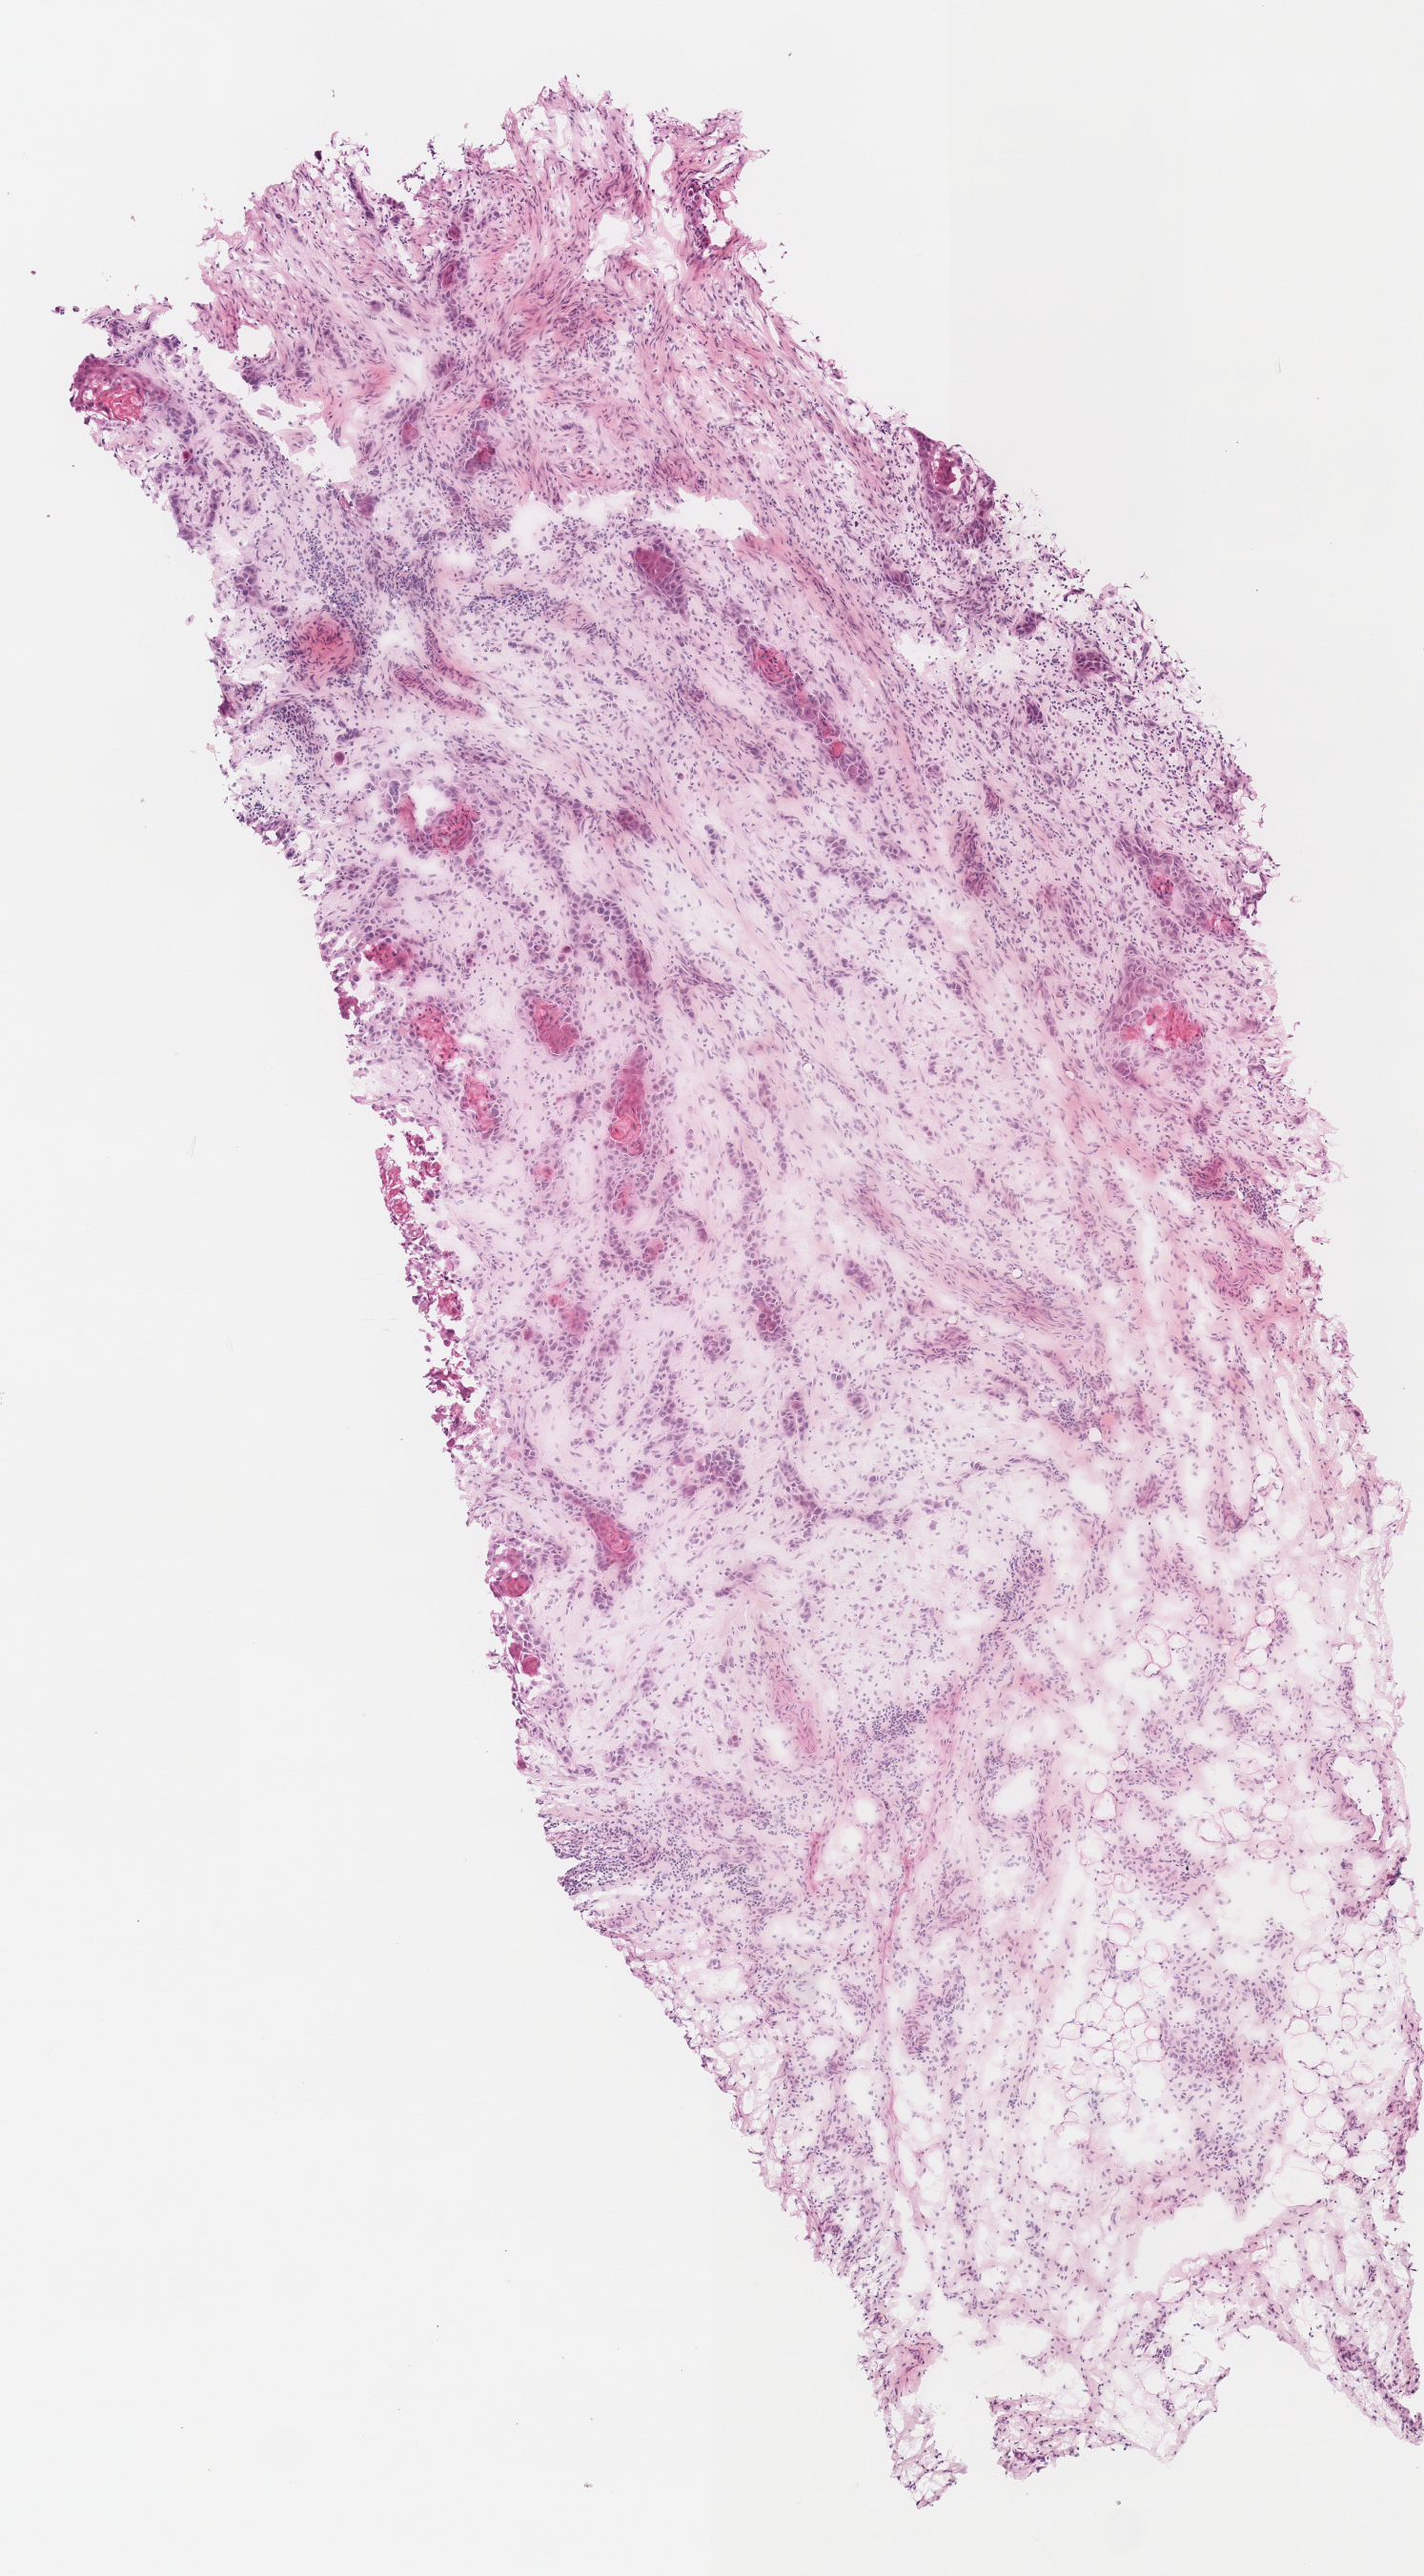
Whole-slide histology image, H&E-stained — a low-resolution overview of the entire scanned area, about 2.9 x 5.3 mm; frozen section; sample: primary tumour, head and neck. Patient: female, age at initial diagnosis 69 years. Histologic grade: G3 (poorly differentiated). Pathologist review of this section (percent, as recorded): tumour cells 90%, tumour nuclei 65%, normal cells 0%, stromal cells 10%, necrosis 0%. Infiltration values recorded for this section: lymphocyte infiltration 20%, monocyte infiltration 0%, neutrophil infiltration 0%.
* pathologic diagnosis: Squamous cell carcinoma, NOS (hypopharynx, NOS)
* AJCC pathologic stage: IVA (6th edition)